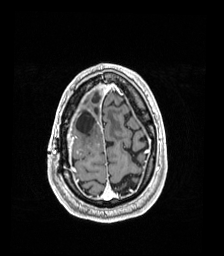
Brain MRI from a brain-tumour surgery series, one axial slice; slice 34 of 192 in the series (ordered by position); T1-weighted post-contrast; 224 × 256 image matrix, field of view 224 × 256 mm. From the clinical record (not read from this slice): histopathology: Astrocytoma; WHO grade: 4; IDH mutation: yes.
Structures marked on this image (manually delineated by an expert):
- previous resection cavity: bounding box (x1, y1, x2, y2) in pixels: (76, 111, 96, 133)
- tumour: (77, 146, 85, 156)